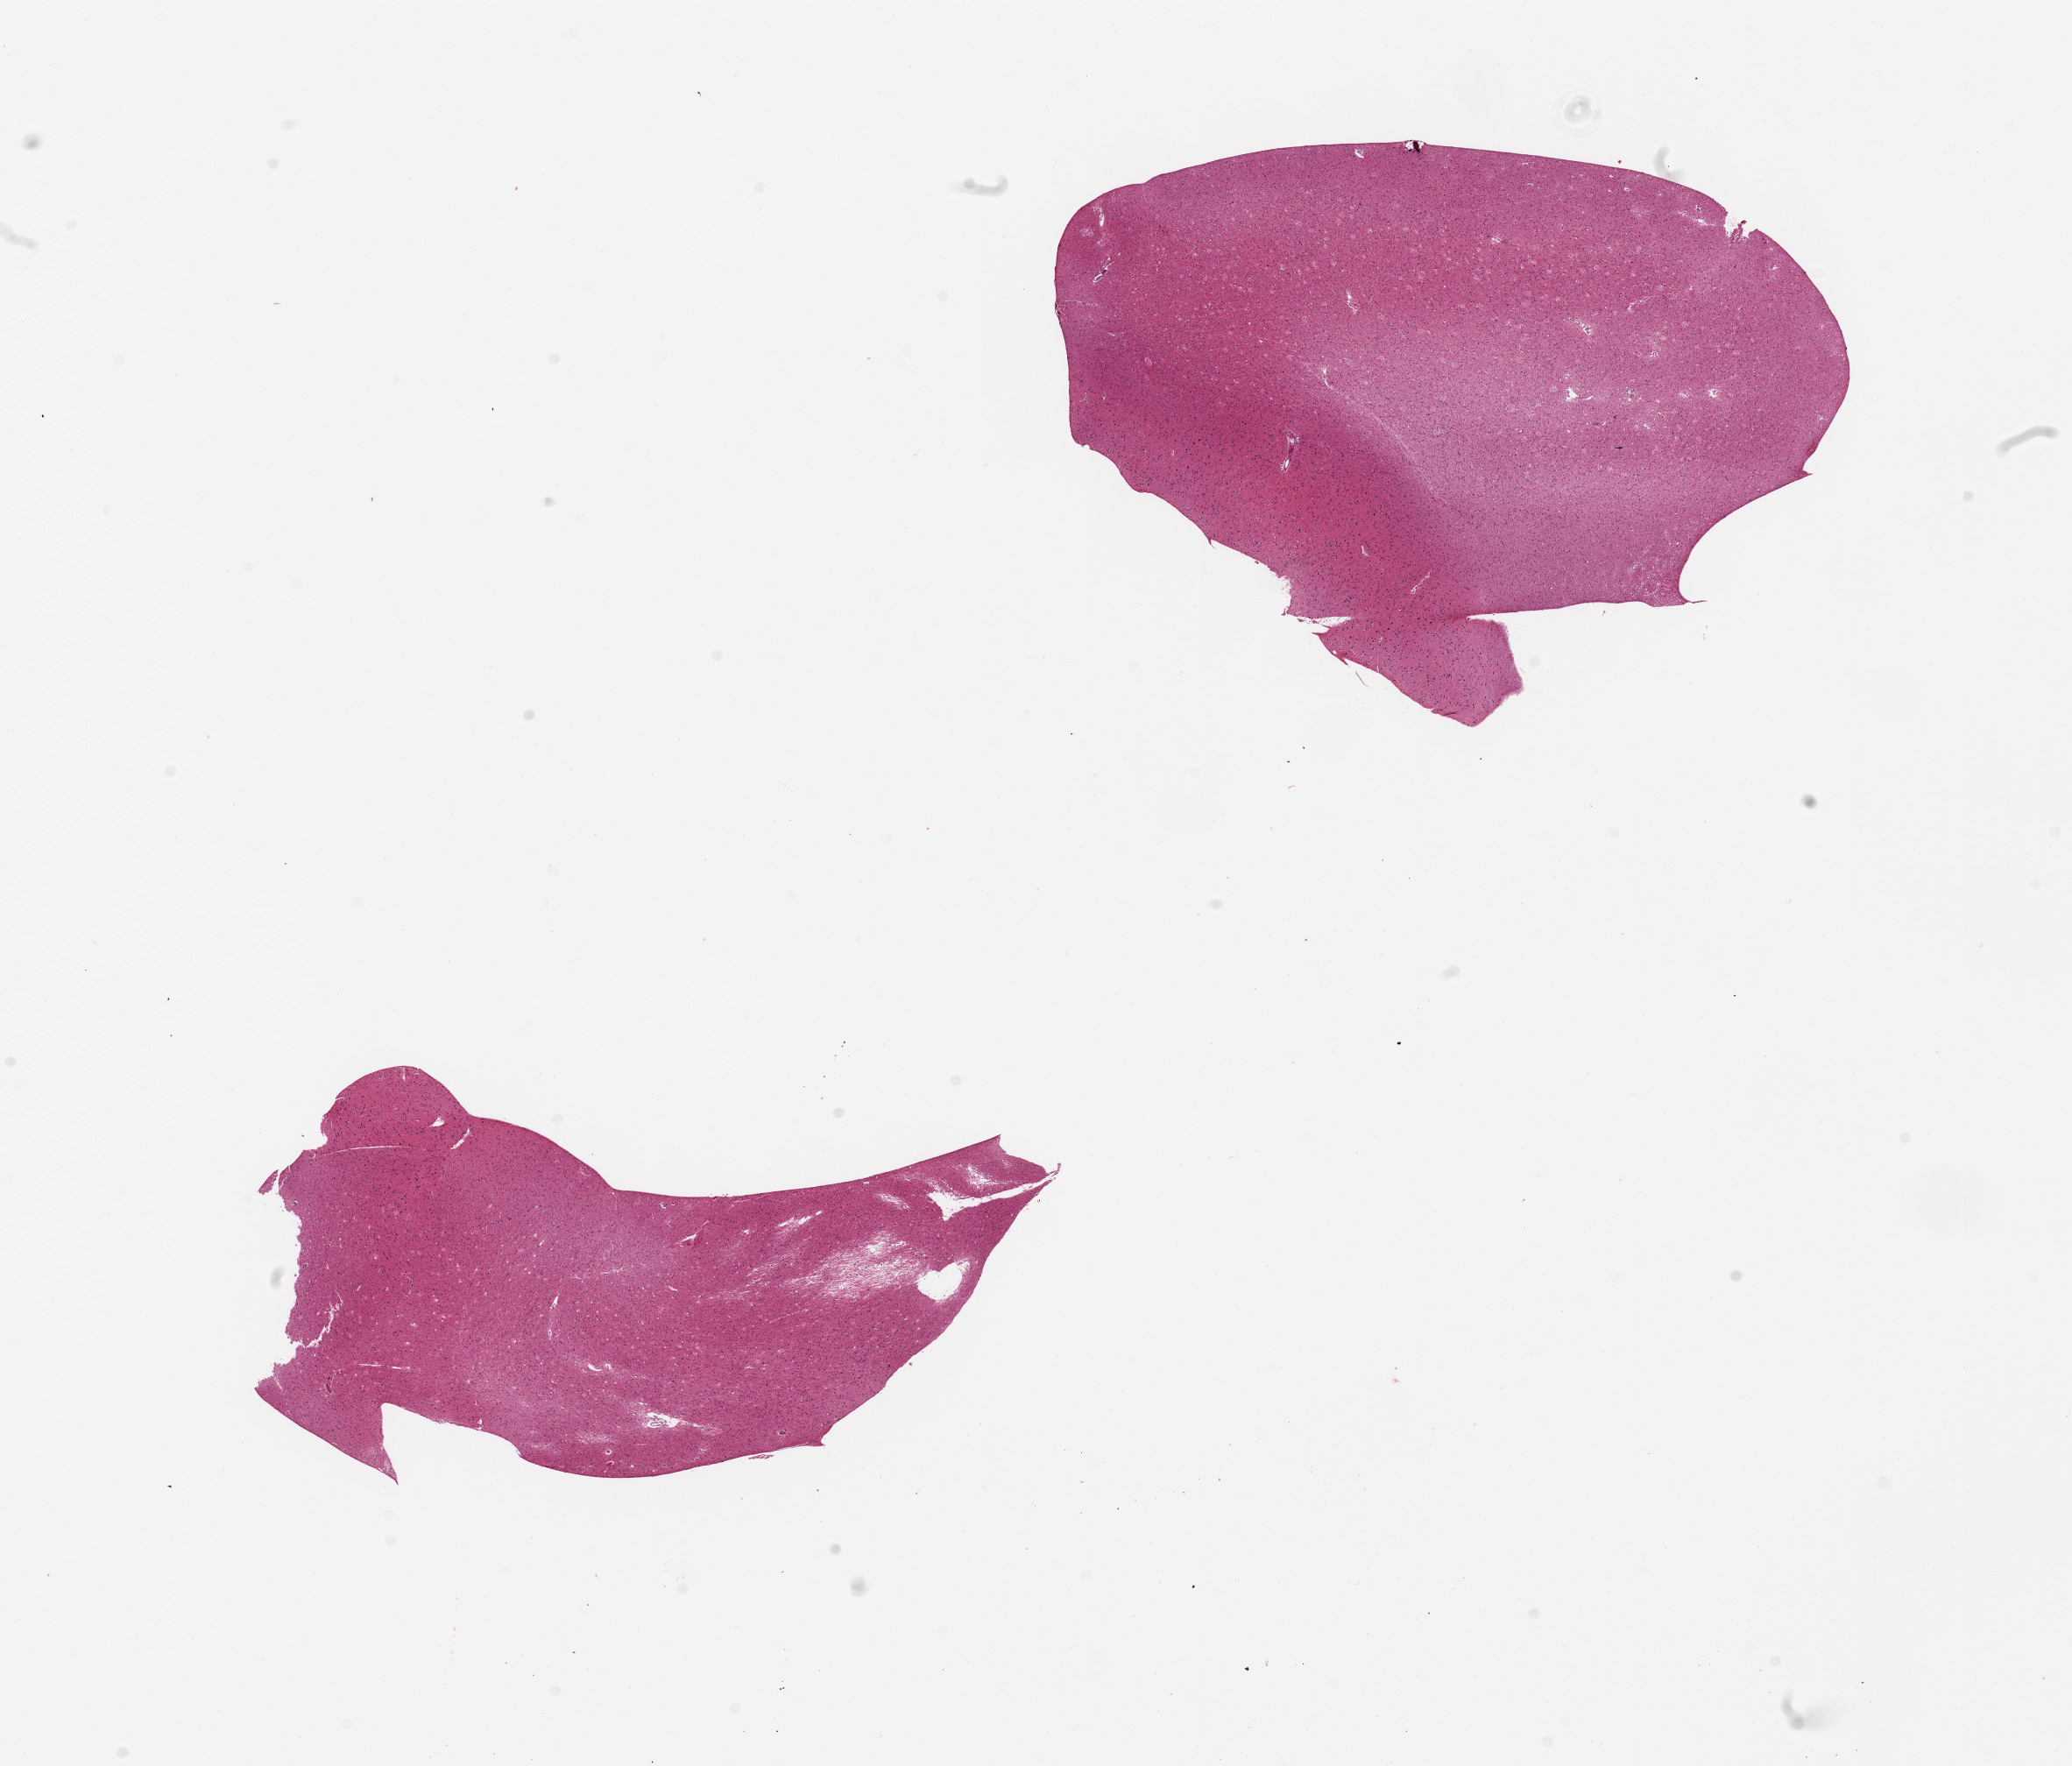
Digitized haematoxylin and eosin-stained section — low-resolution overview of the scanned area, about 18.7 x 15.9 mm; PAXgene-fixed, paraffin-embedded tissue; section of cerebral cortex (target tissue); tissue donor sample. Female donor.
• pathologist's review note for this sample: 2 pieces